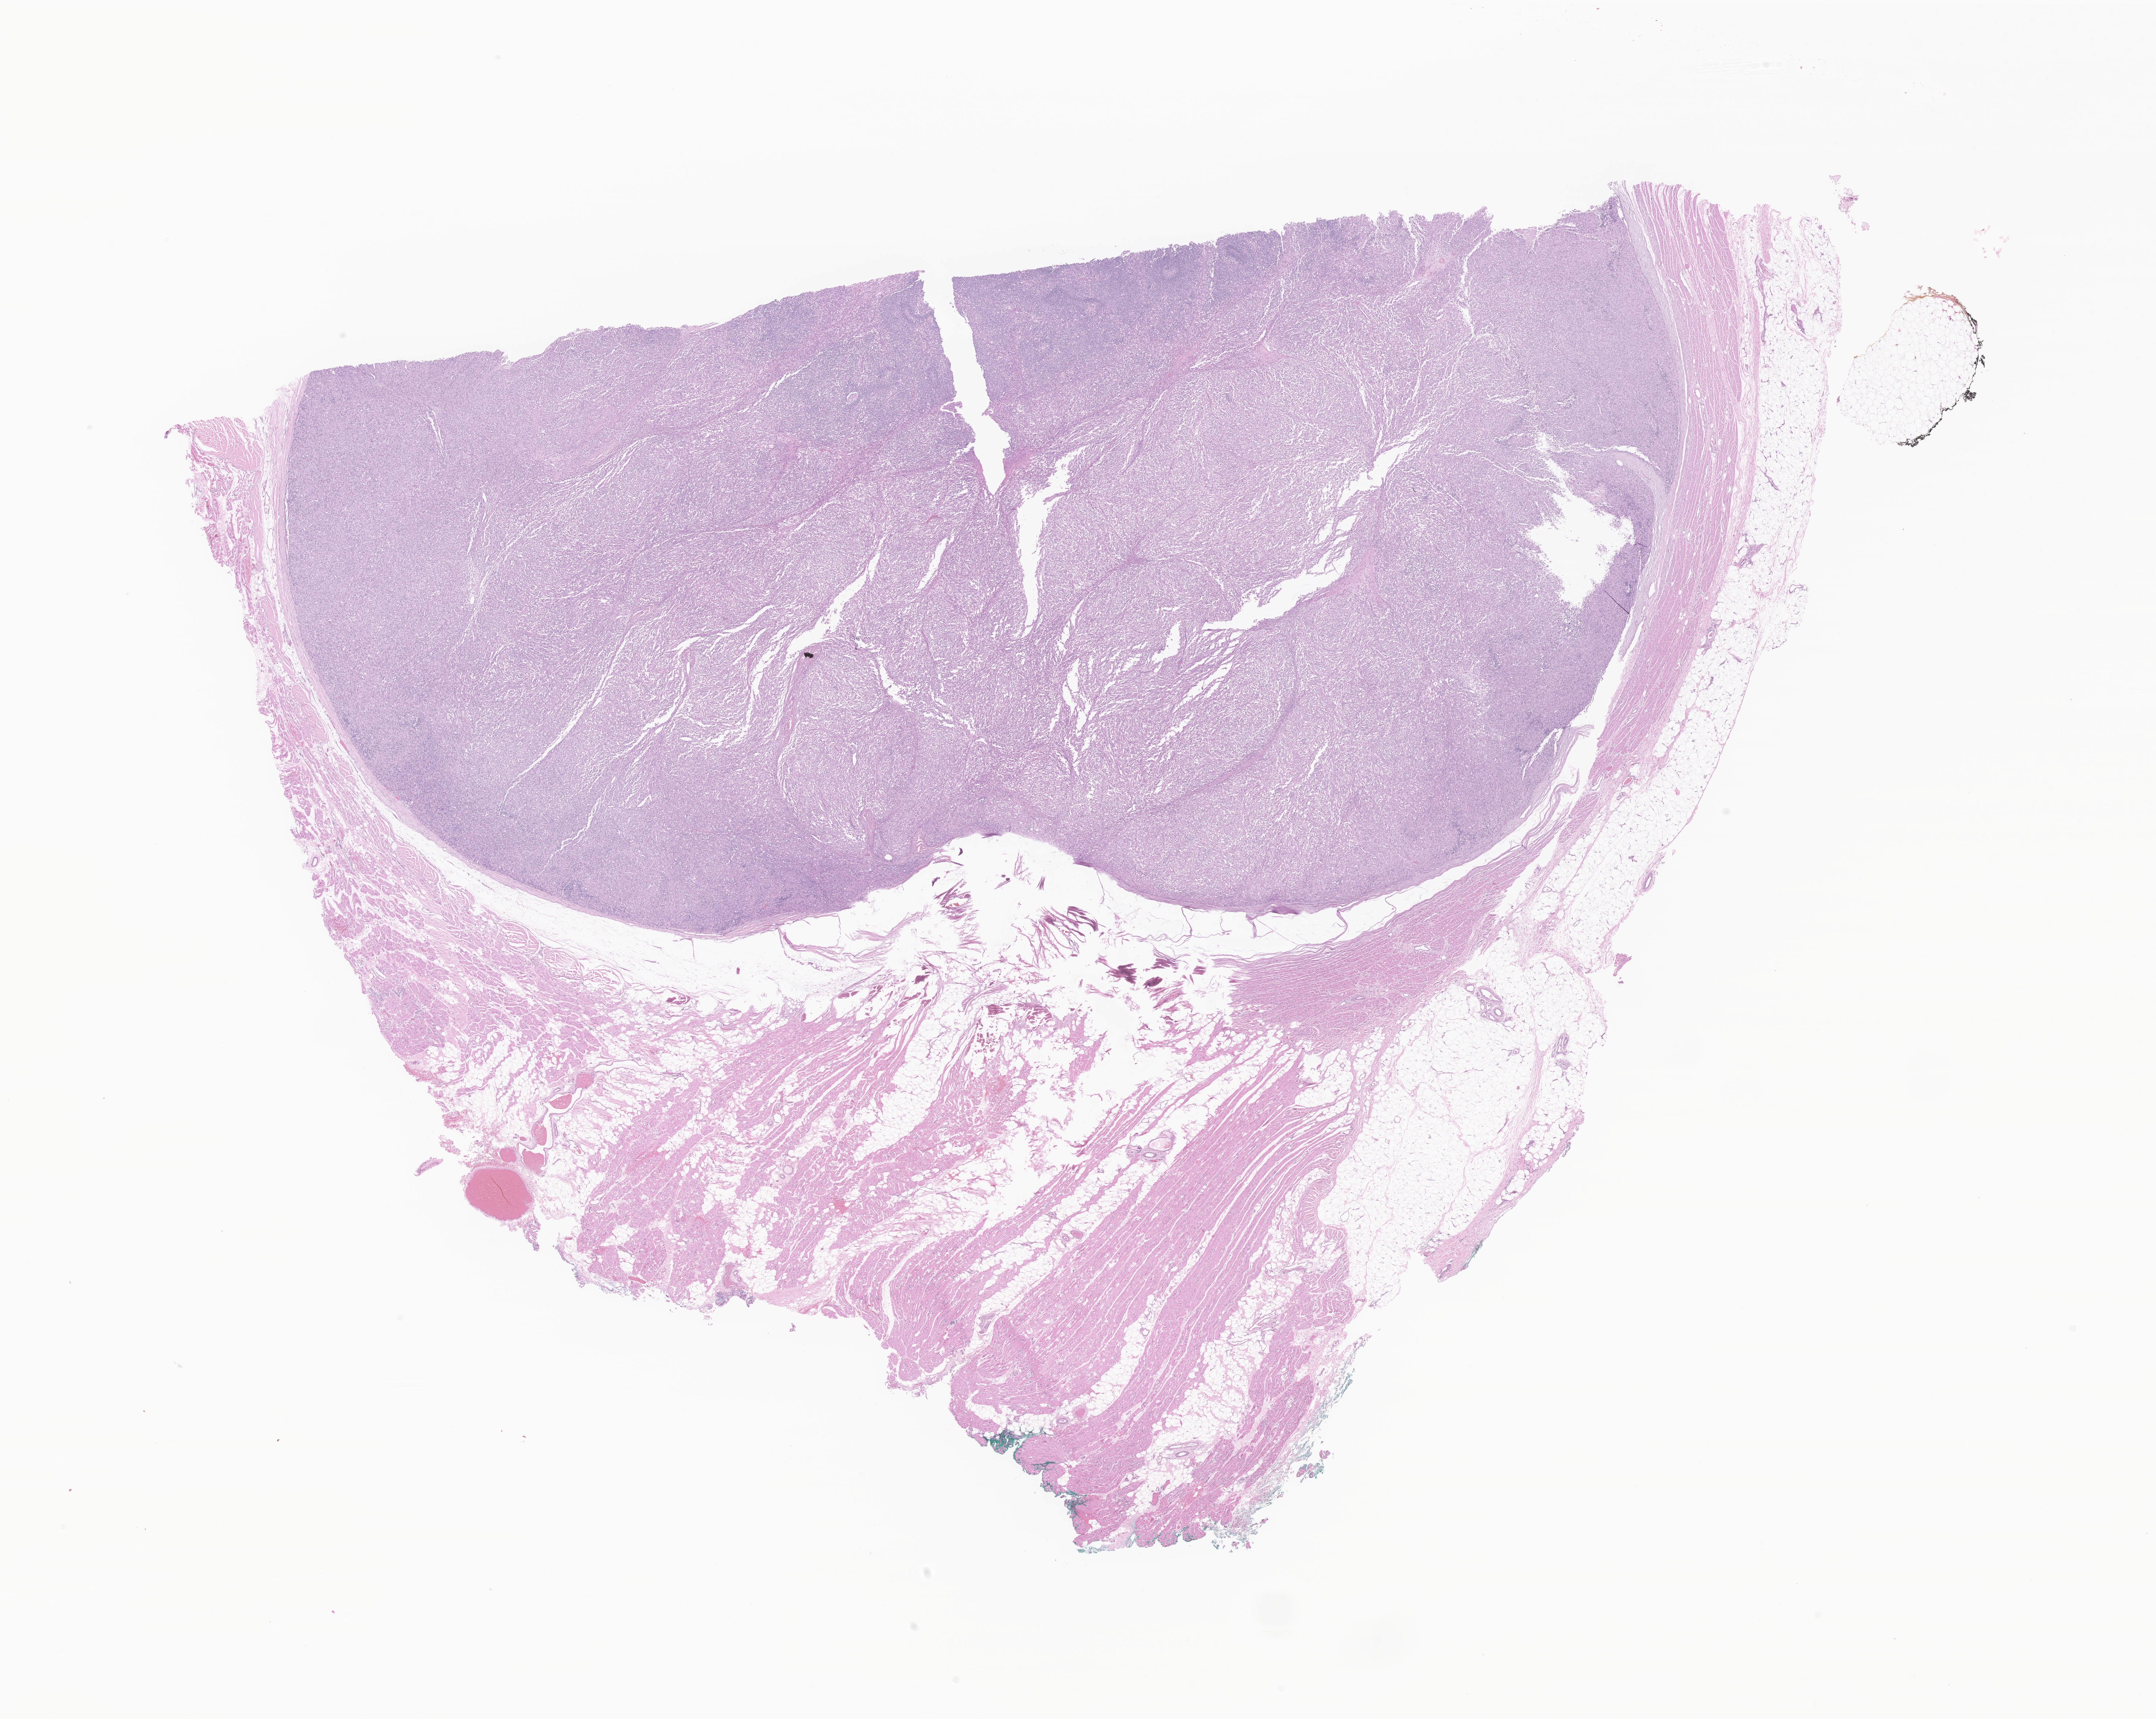
Whole-slide image, haematoxylin and eosin stain of tumor tissue from the soft tissue of lower extremity — whole scanned area (about 24.9 x 19.9 mm) shown as a low-resolution overview, formalin-fixed, paraffin-embedded (FFPE) tissue. Patient: female, age 219 days.
- diagnosis (ICD-O-3 morphology term): Embryonal rhabdomyosarcoma, NOS